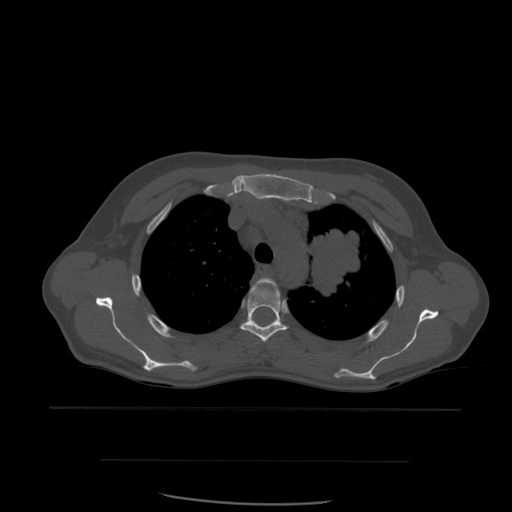
CT including the spine, one axial slice. Bone window (W 1800 / L 400 HU). 1.25 mm slice thickness. 512 × 512 image matrix, field of view 392 × 392 mm. Patient age 48 years. Case-level facts recorded for this patient, not image findings: primary cancer: lung.
Structures marked on this image (semi-automatic segmentation, software-assisted and operator-edited):
- T3 vertebra: bounding box (x1, y1, x2, y2) in pixels: (251, 278, 280, 295)
- T4 vertebra: (240, 286, 288, 343)